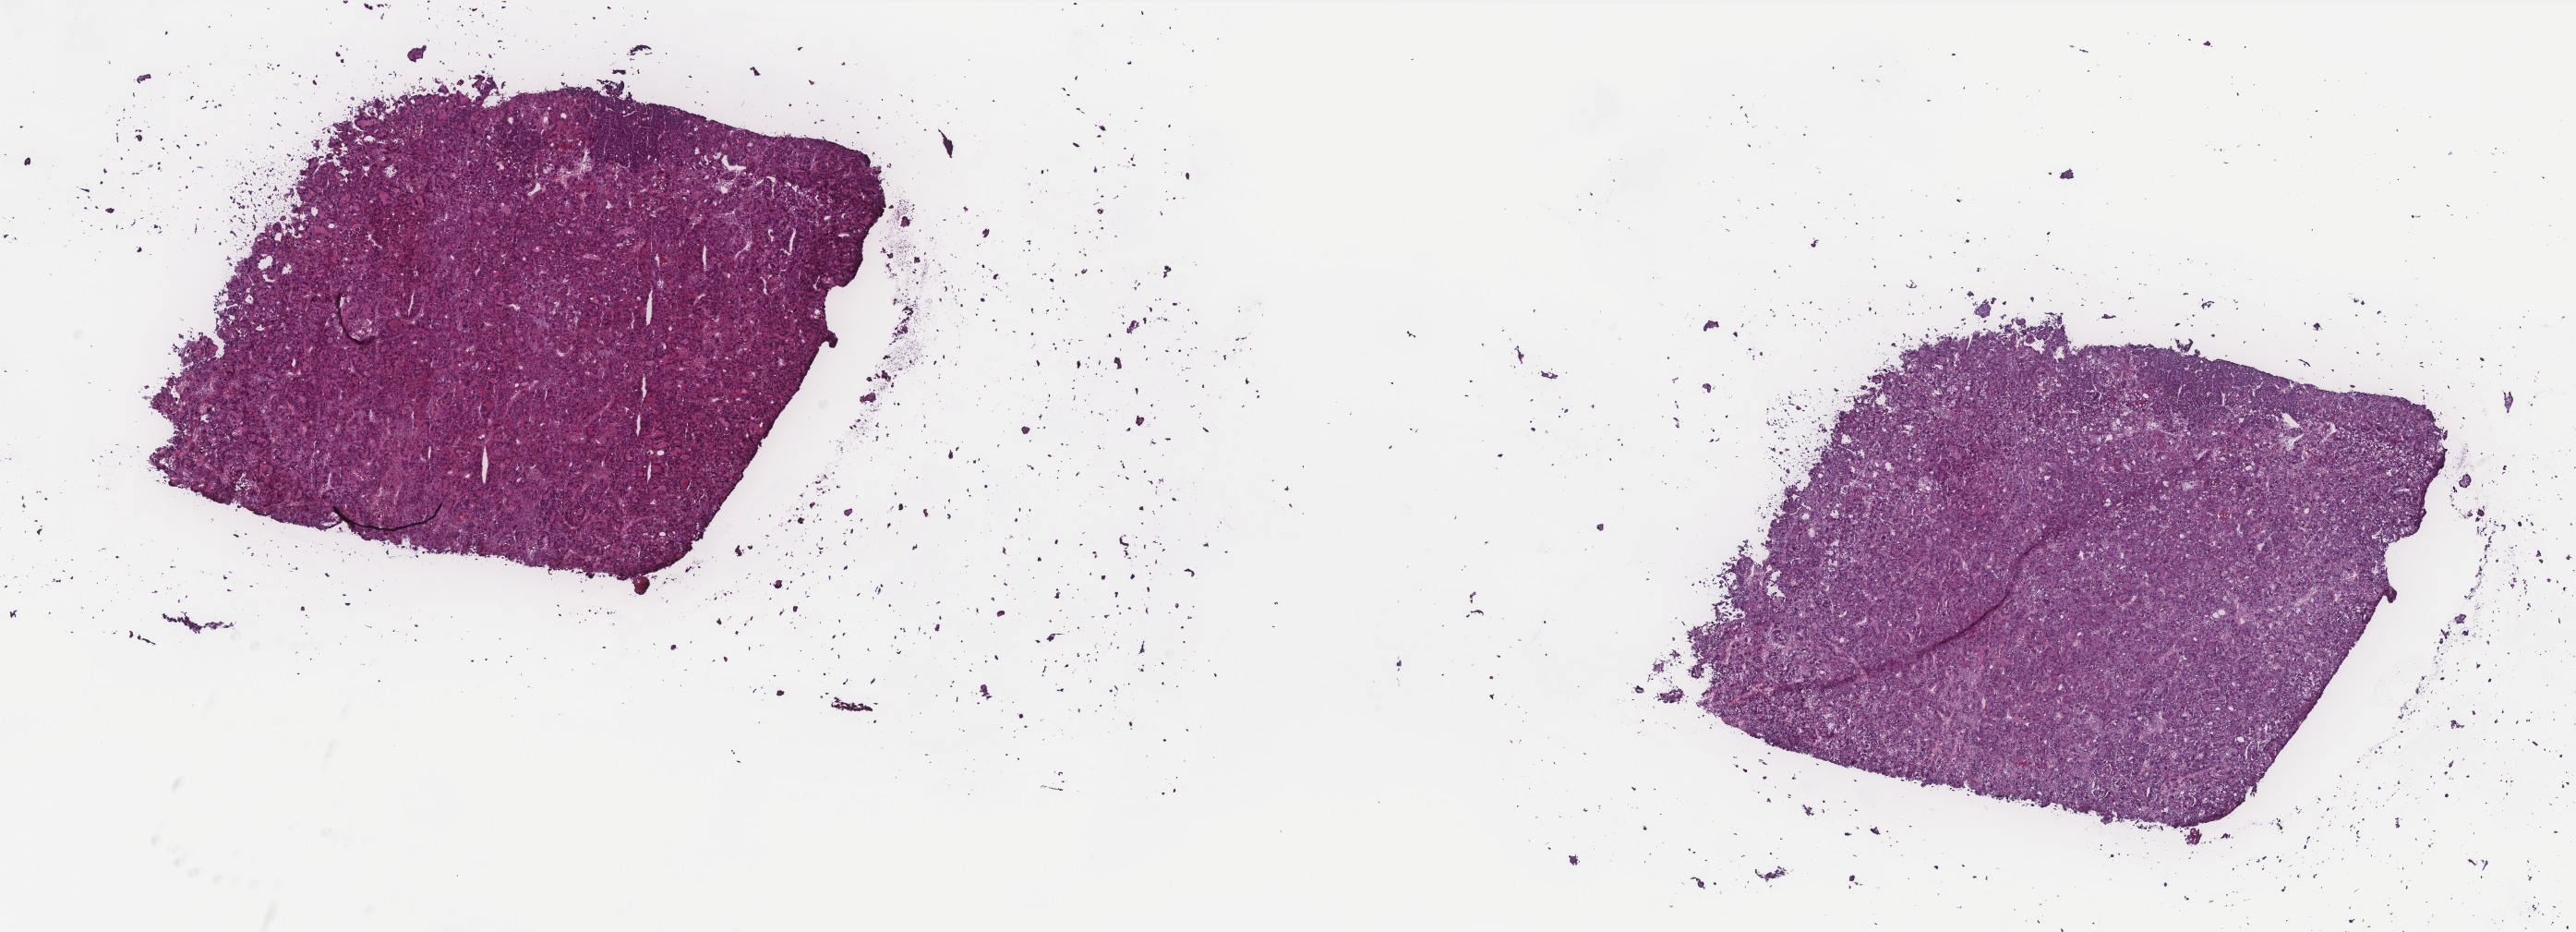
Whole-slide histology image, H&E-stained — whole scanned area (about 22.4 x 8.1 mm, from a 40x scan) shown as a low-resolution overview; frozen section from the top of the tissue portion; sample: primary tumour, liver. Male patient; age at initial diagnosis 73 years.
Diagnosis: Hepatocellular carcinoma, NOS.